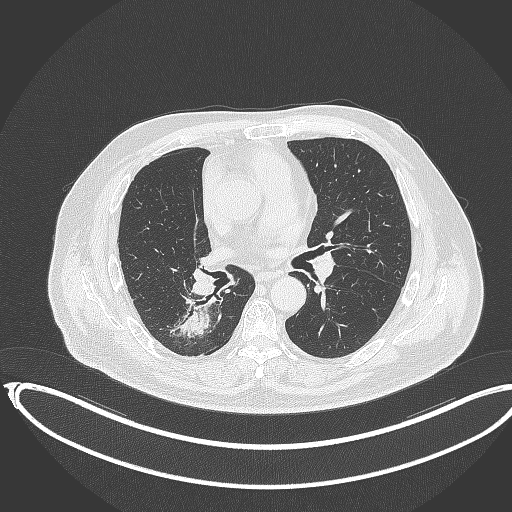
Chest CT, one axial slice; slice 186 of 403 in the series (ordered by position); reconstruction kernel B70f; 120 kVp; lung window (W 1500 / L -600 HU); 512 × 512 image matrix, field of view 436 × 436 mm. Male patient, age 68 years. From the clinical record (not read from this slice): clinical TNM (as recorded): T2a N0 M0.
Structures marked on this image (bounding box drawn by a radiologist):
- lung tumour (recorded histology: adenocarcinoma): box from (x=168, y=291) to (x=214, y=337) px